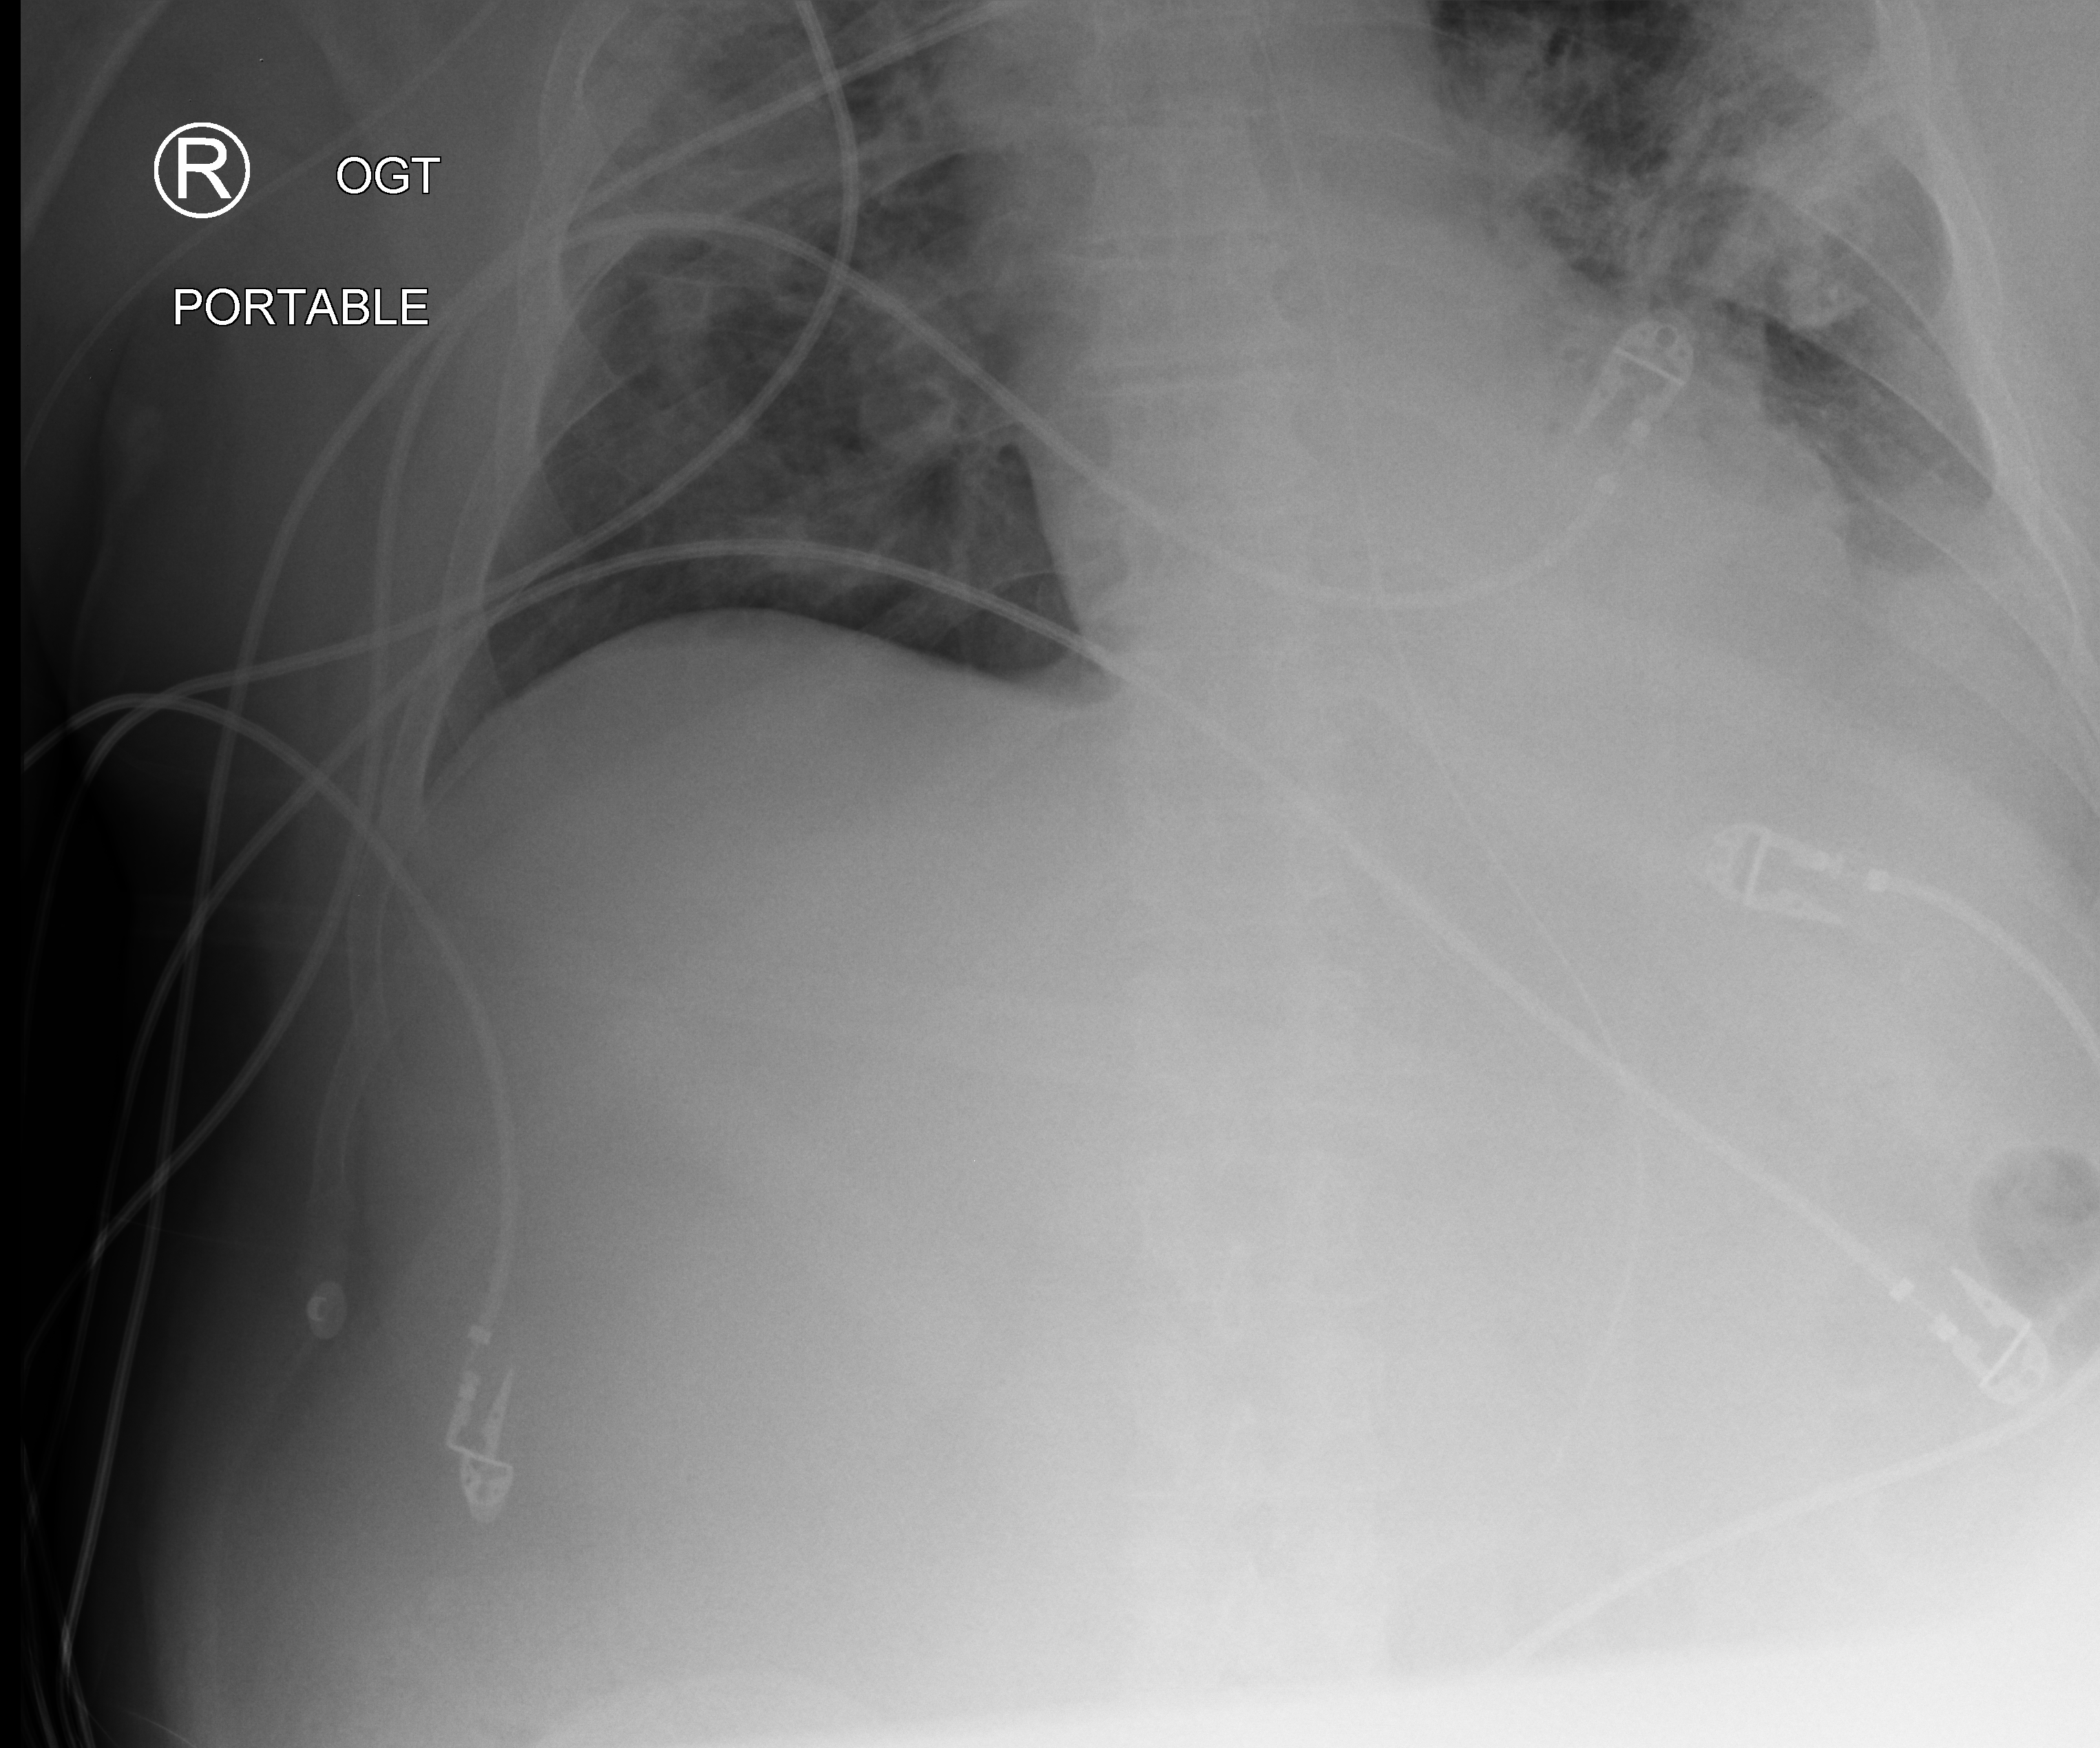
Portable chest radiograph, anteroposterior (AP) projection. Male patient hospitalised with COVID-19, age 60–74 years.
From the hospital-stay record, not from the radiograph (when in the stay this image was taken is not recorded): mechanically ventilated during this hospital stay: yes; admitted to intensive care during this hospital stay: yes.